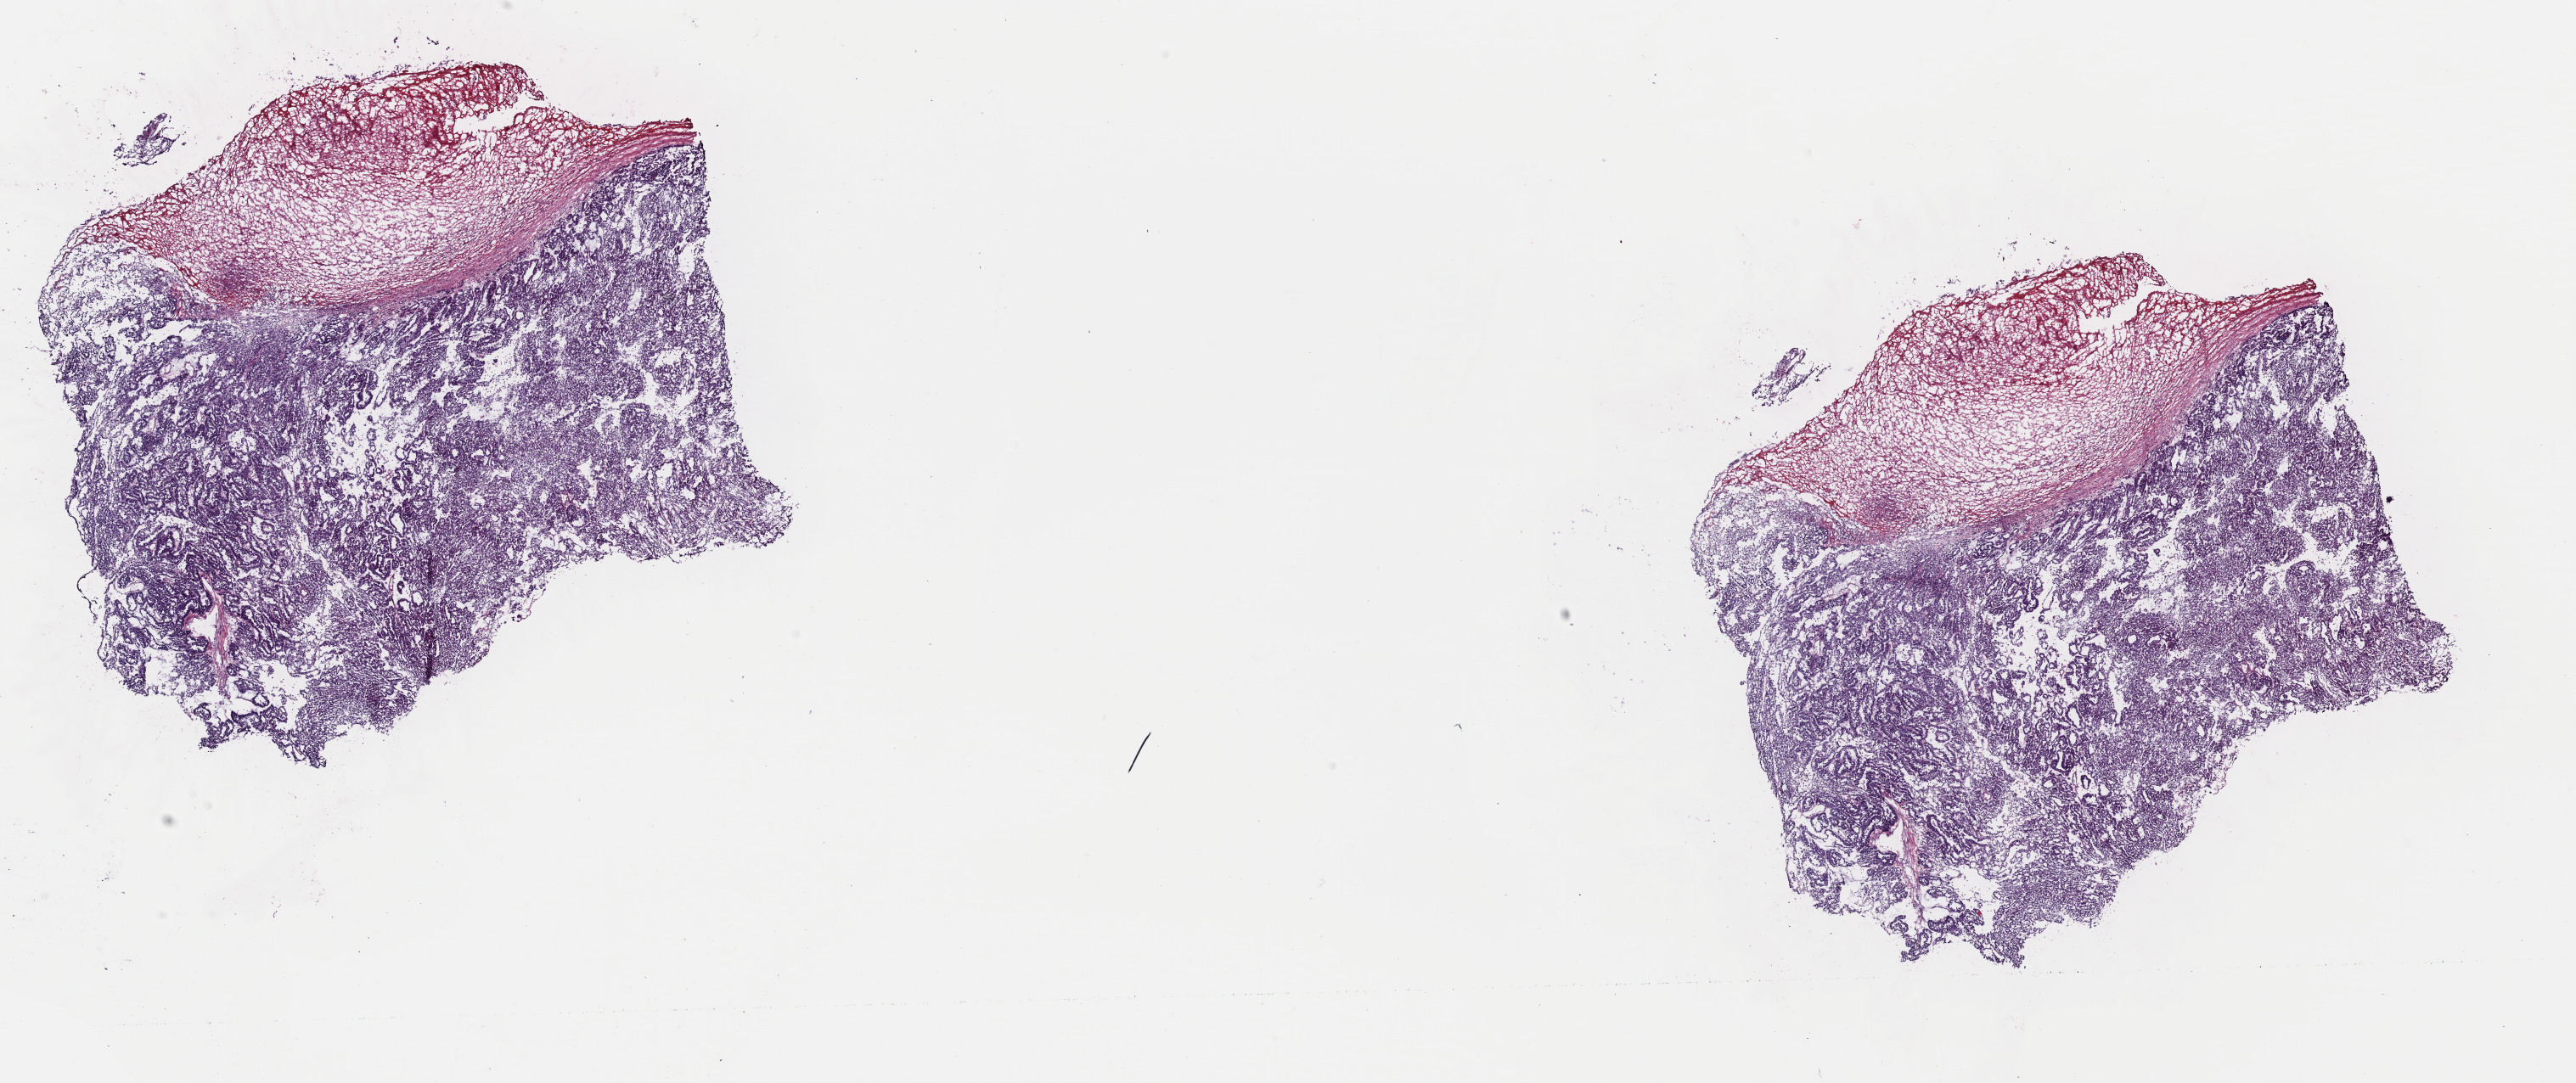
Digitized Hematoxylin and eosin (H&E) stained tissue section (whole slide) — whole scanned area (about 24.0 x 10.1 mm) shown as a low-resolution overview; frozen section from the top of the tissue portion; sample: primary tumour, kidney. Female, age 60 years at initial diagnosis. Slide review estimates, as recorded: tumour cells 85%, tumour nuclei 90%, normal cells 0%, stromal cells 15%, necrosis 0%. Inflammatory infiltration, as recorded: lymphocyte infiltration 0%, monocyte infiltration 0%, neutrophil infiltration 0%.
Lymph nodes positive (case pathology): 2 of 7 examined. TNM: T3a N1 MX. Histologic diagnosis: Papillary adenocarcinoma, NOS. AJCC pathologic stage: III (7th edition).